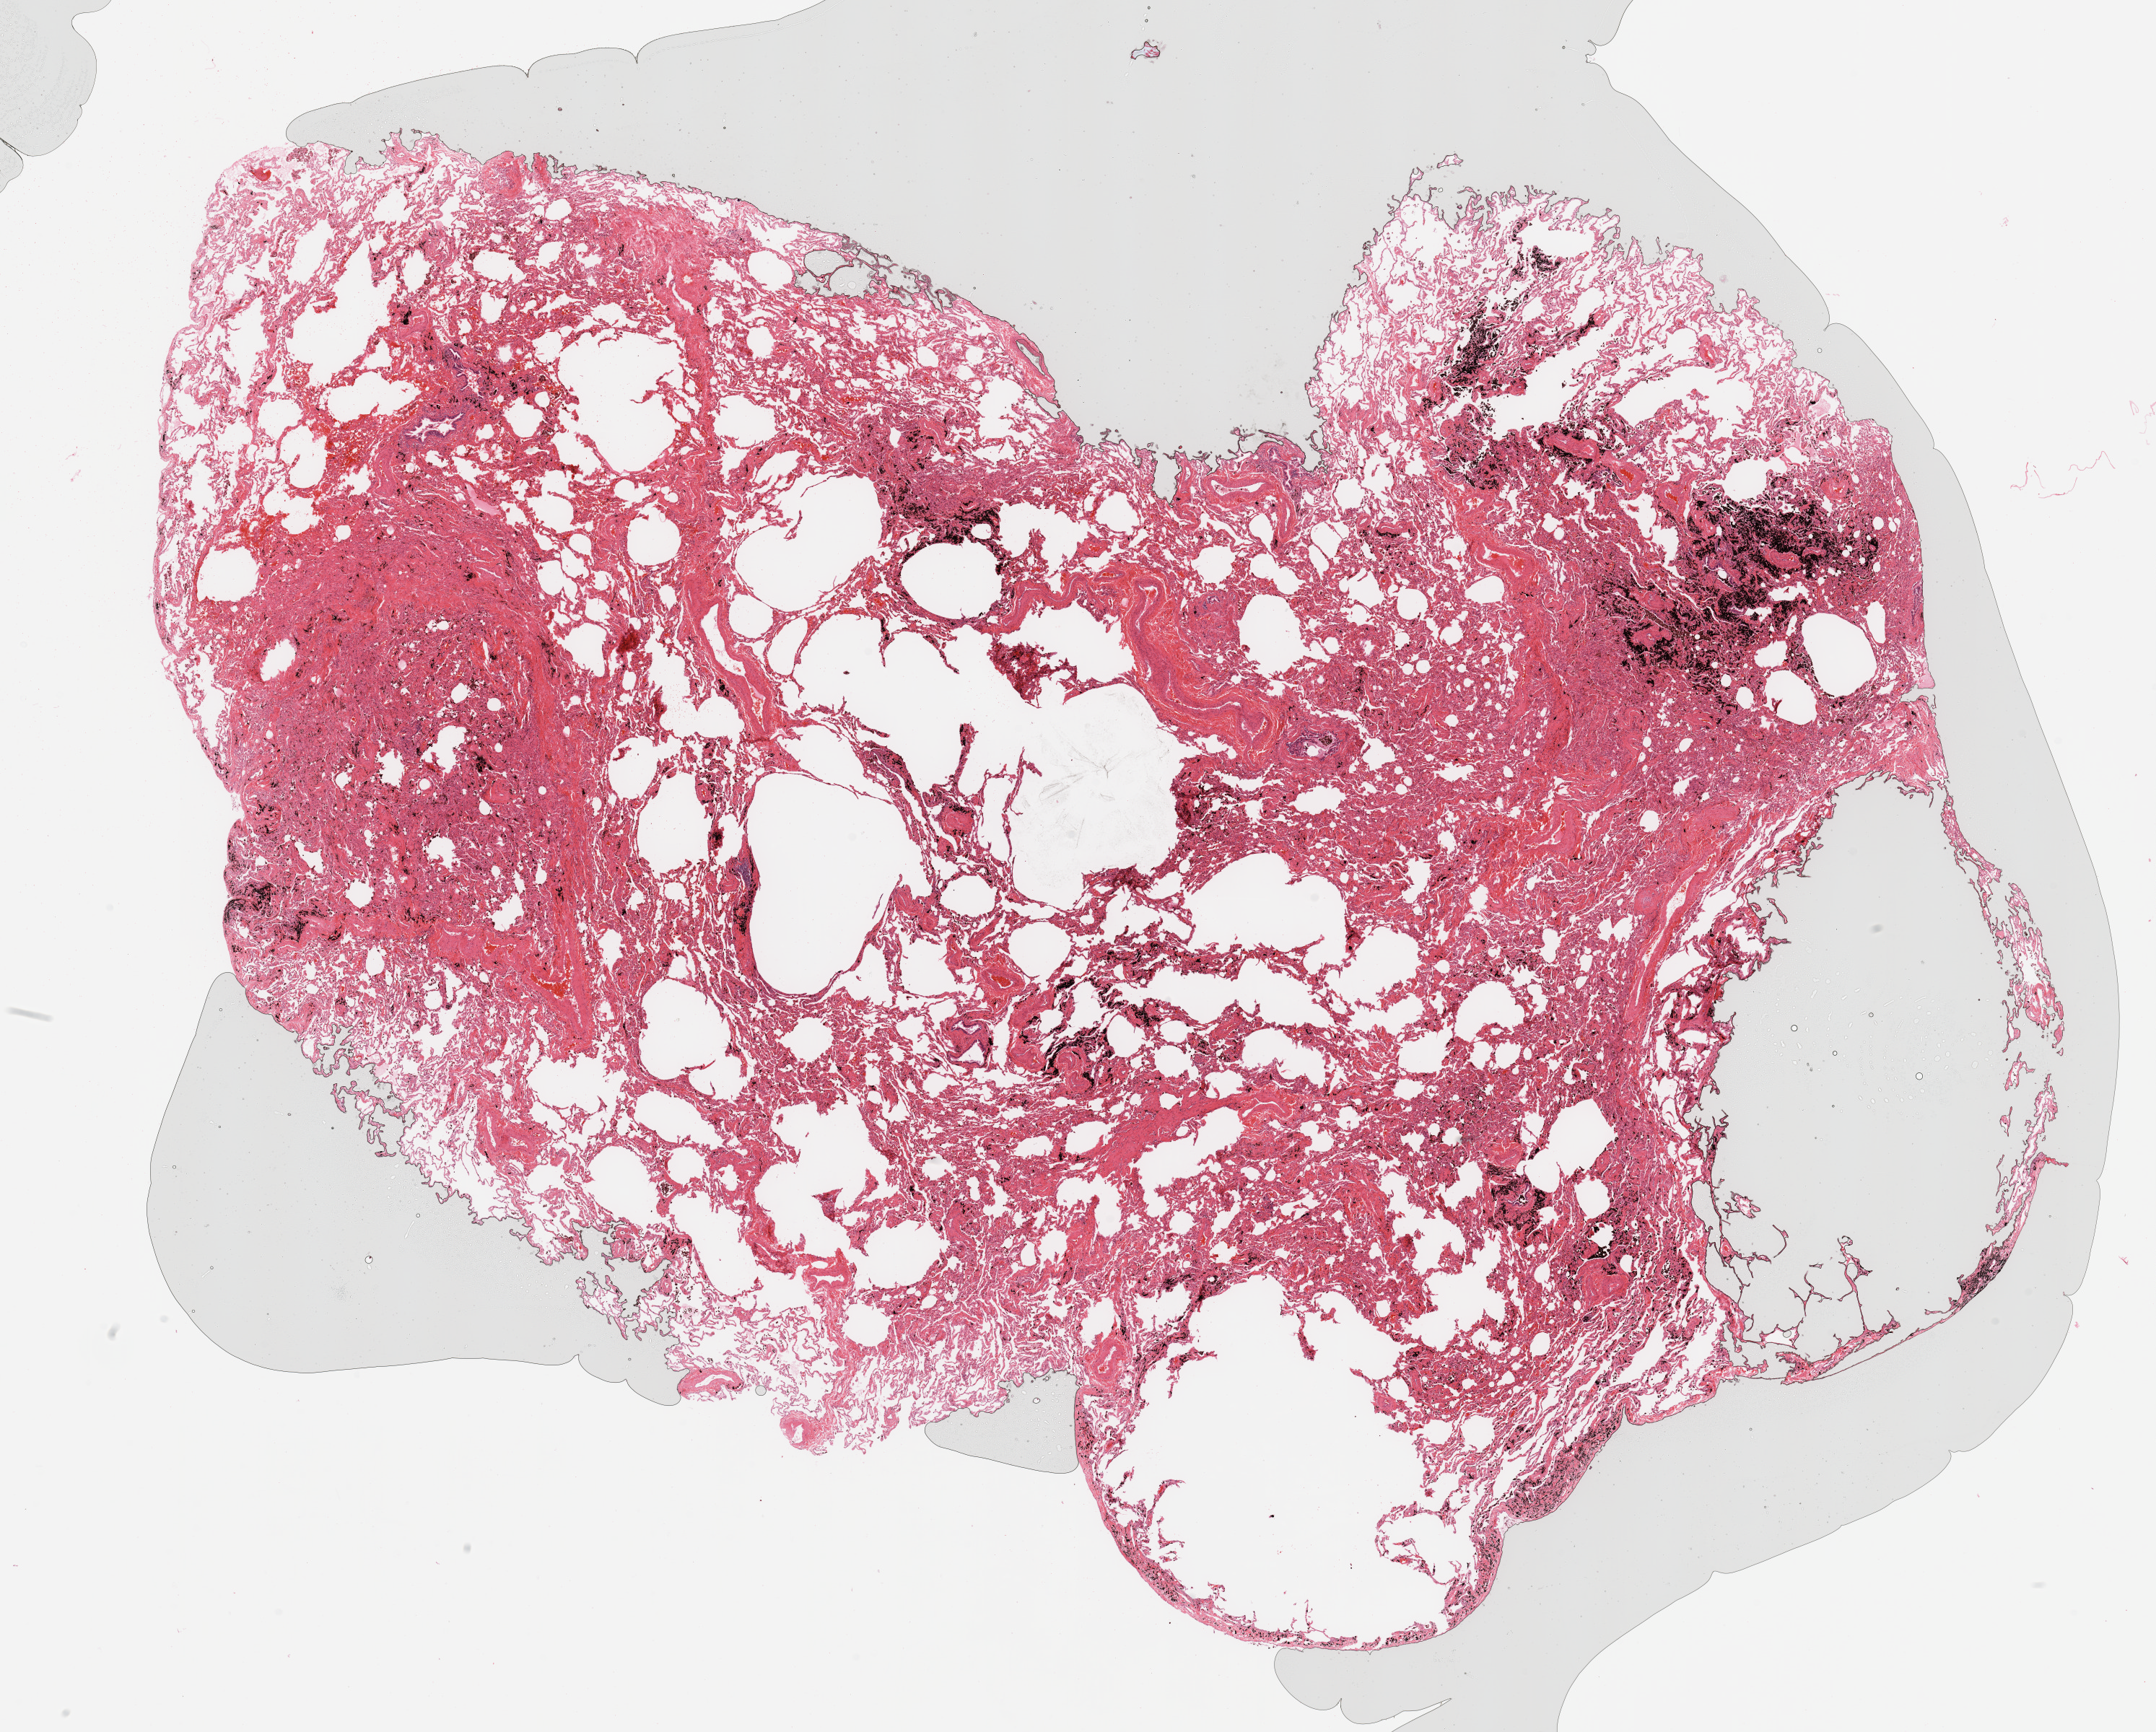
Whole-slide histology image, Hematoxylin and eosin (H&E) stained — low-resolution overview of the scanned area, about 23.6 x 19.0 mm; lung, normal (non-tumour) tissue. Male, 64 y/o.
This section: normal (non-tumour) tissue from the same patient. Patient diagnosis (cohort enrolment): squamous cell carcinoma (lung).